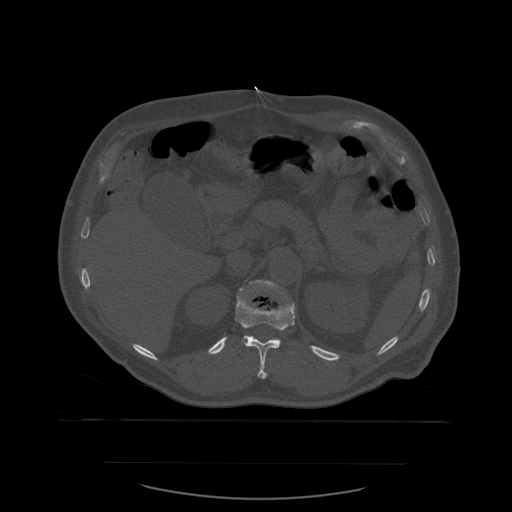
CT including the spine, one axial slice. Slice 267 of 590 in the series (ordered by position). Bone window (W 1800 / L 400 HU). 512 × 512 image matrix, field of view 479 × 479 mm. Patient age 71 years. From the clinical record (not read from this slice): primary cancer: lung; vertebrae with lytic lesions (as recorded): T1, T2, L5, S1.
Annotated regions visible in this slice (semi-automatic segmentation, software-assisted and operator-edited):
- L1 vertebra: bounding box <251,280,295,307> (left, top, right, bottom; pixels)
- T12 vertebra: <235,283,295,379>